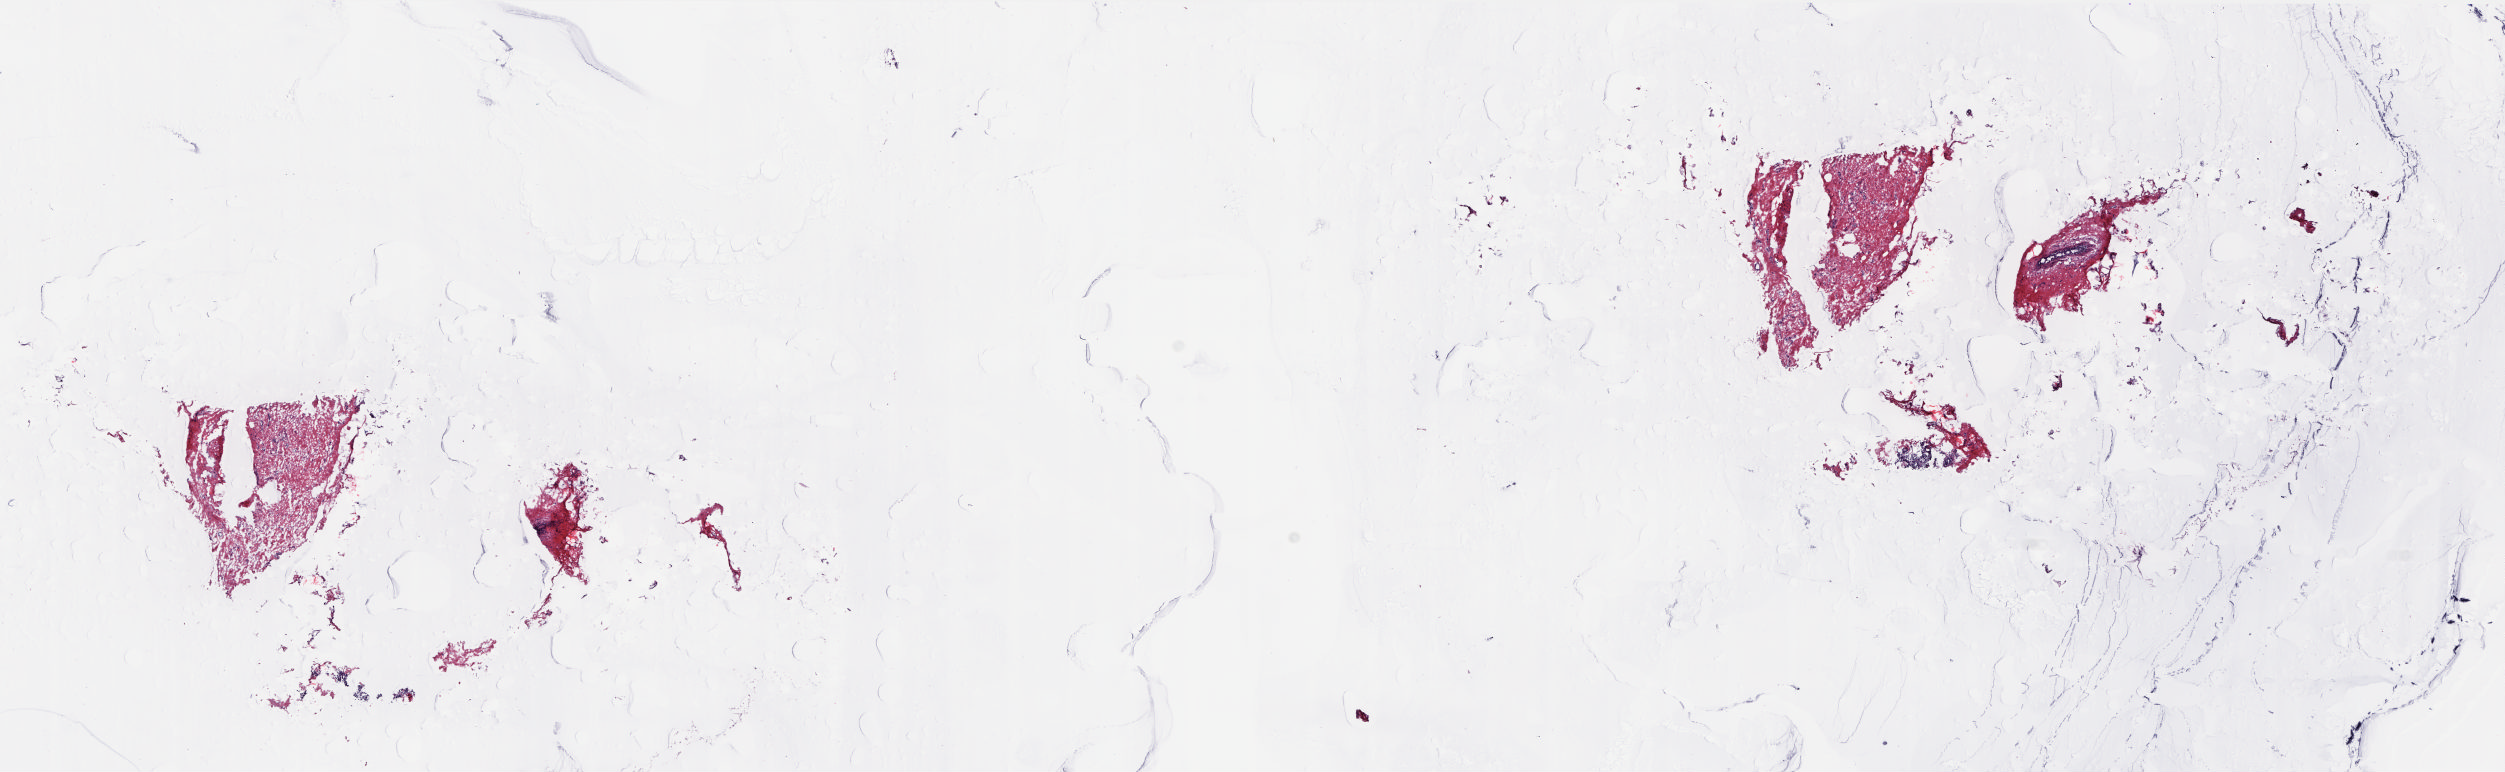
H&E whole-slide image — low-resolution overview of the scanned area, about 20.2 x 6.2 mm (from a 20x scan). Frozen section. Solid tissue normal (non-tumour tissue) sample from the breast. Female, age 52 years at initial diagnosis. Slide review estimates, as recorded: tumour cells 0%, tumour nuclei 0%, normal cells 5%, stromal cells 95%, necrosis 0%. Infiltration values recorded for this section: lymphocyte infiltration 1%, monocyte infiltration 0%, neutrophil infiltration 0%.
* this section: solid tissue normal (non-tumour) sample from the same patient
* patient diagnosis: Infiltrating duct carcinoma, NOS